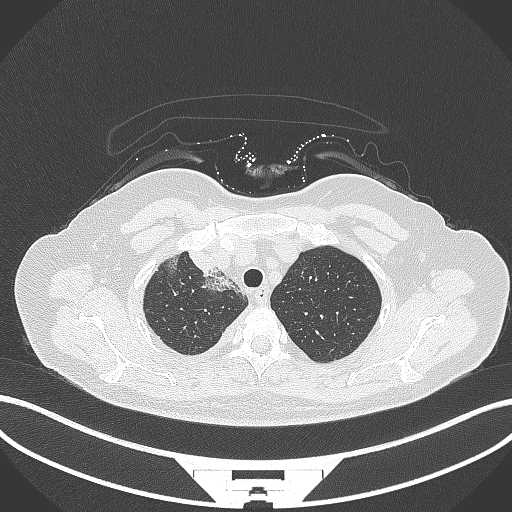
Chest CT, one axial slice. Reconstruction kernel B70f. 120 kVp. Lung window (W 1500 / L -600 HU). 1 mm slice thickness. 512 × 512 image matrix. Female patient, age 52 years. From the clinical record (not read from this slice): clinical TNM (as recorded): T3 N1 M1.
Structures marked on this image (rectangle marked by the reading radiologist):
- lung tumour (recorded histology: adenocarcinoma): bounding box [x1, y1, x2, y2] px = [184, 246, 219, 281]